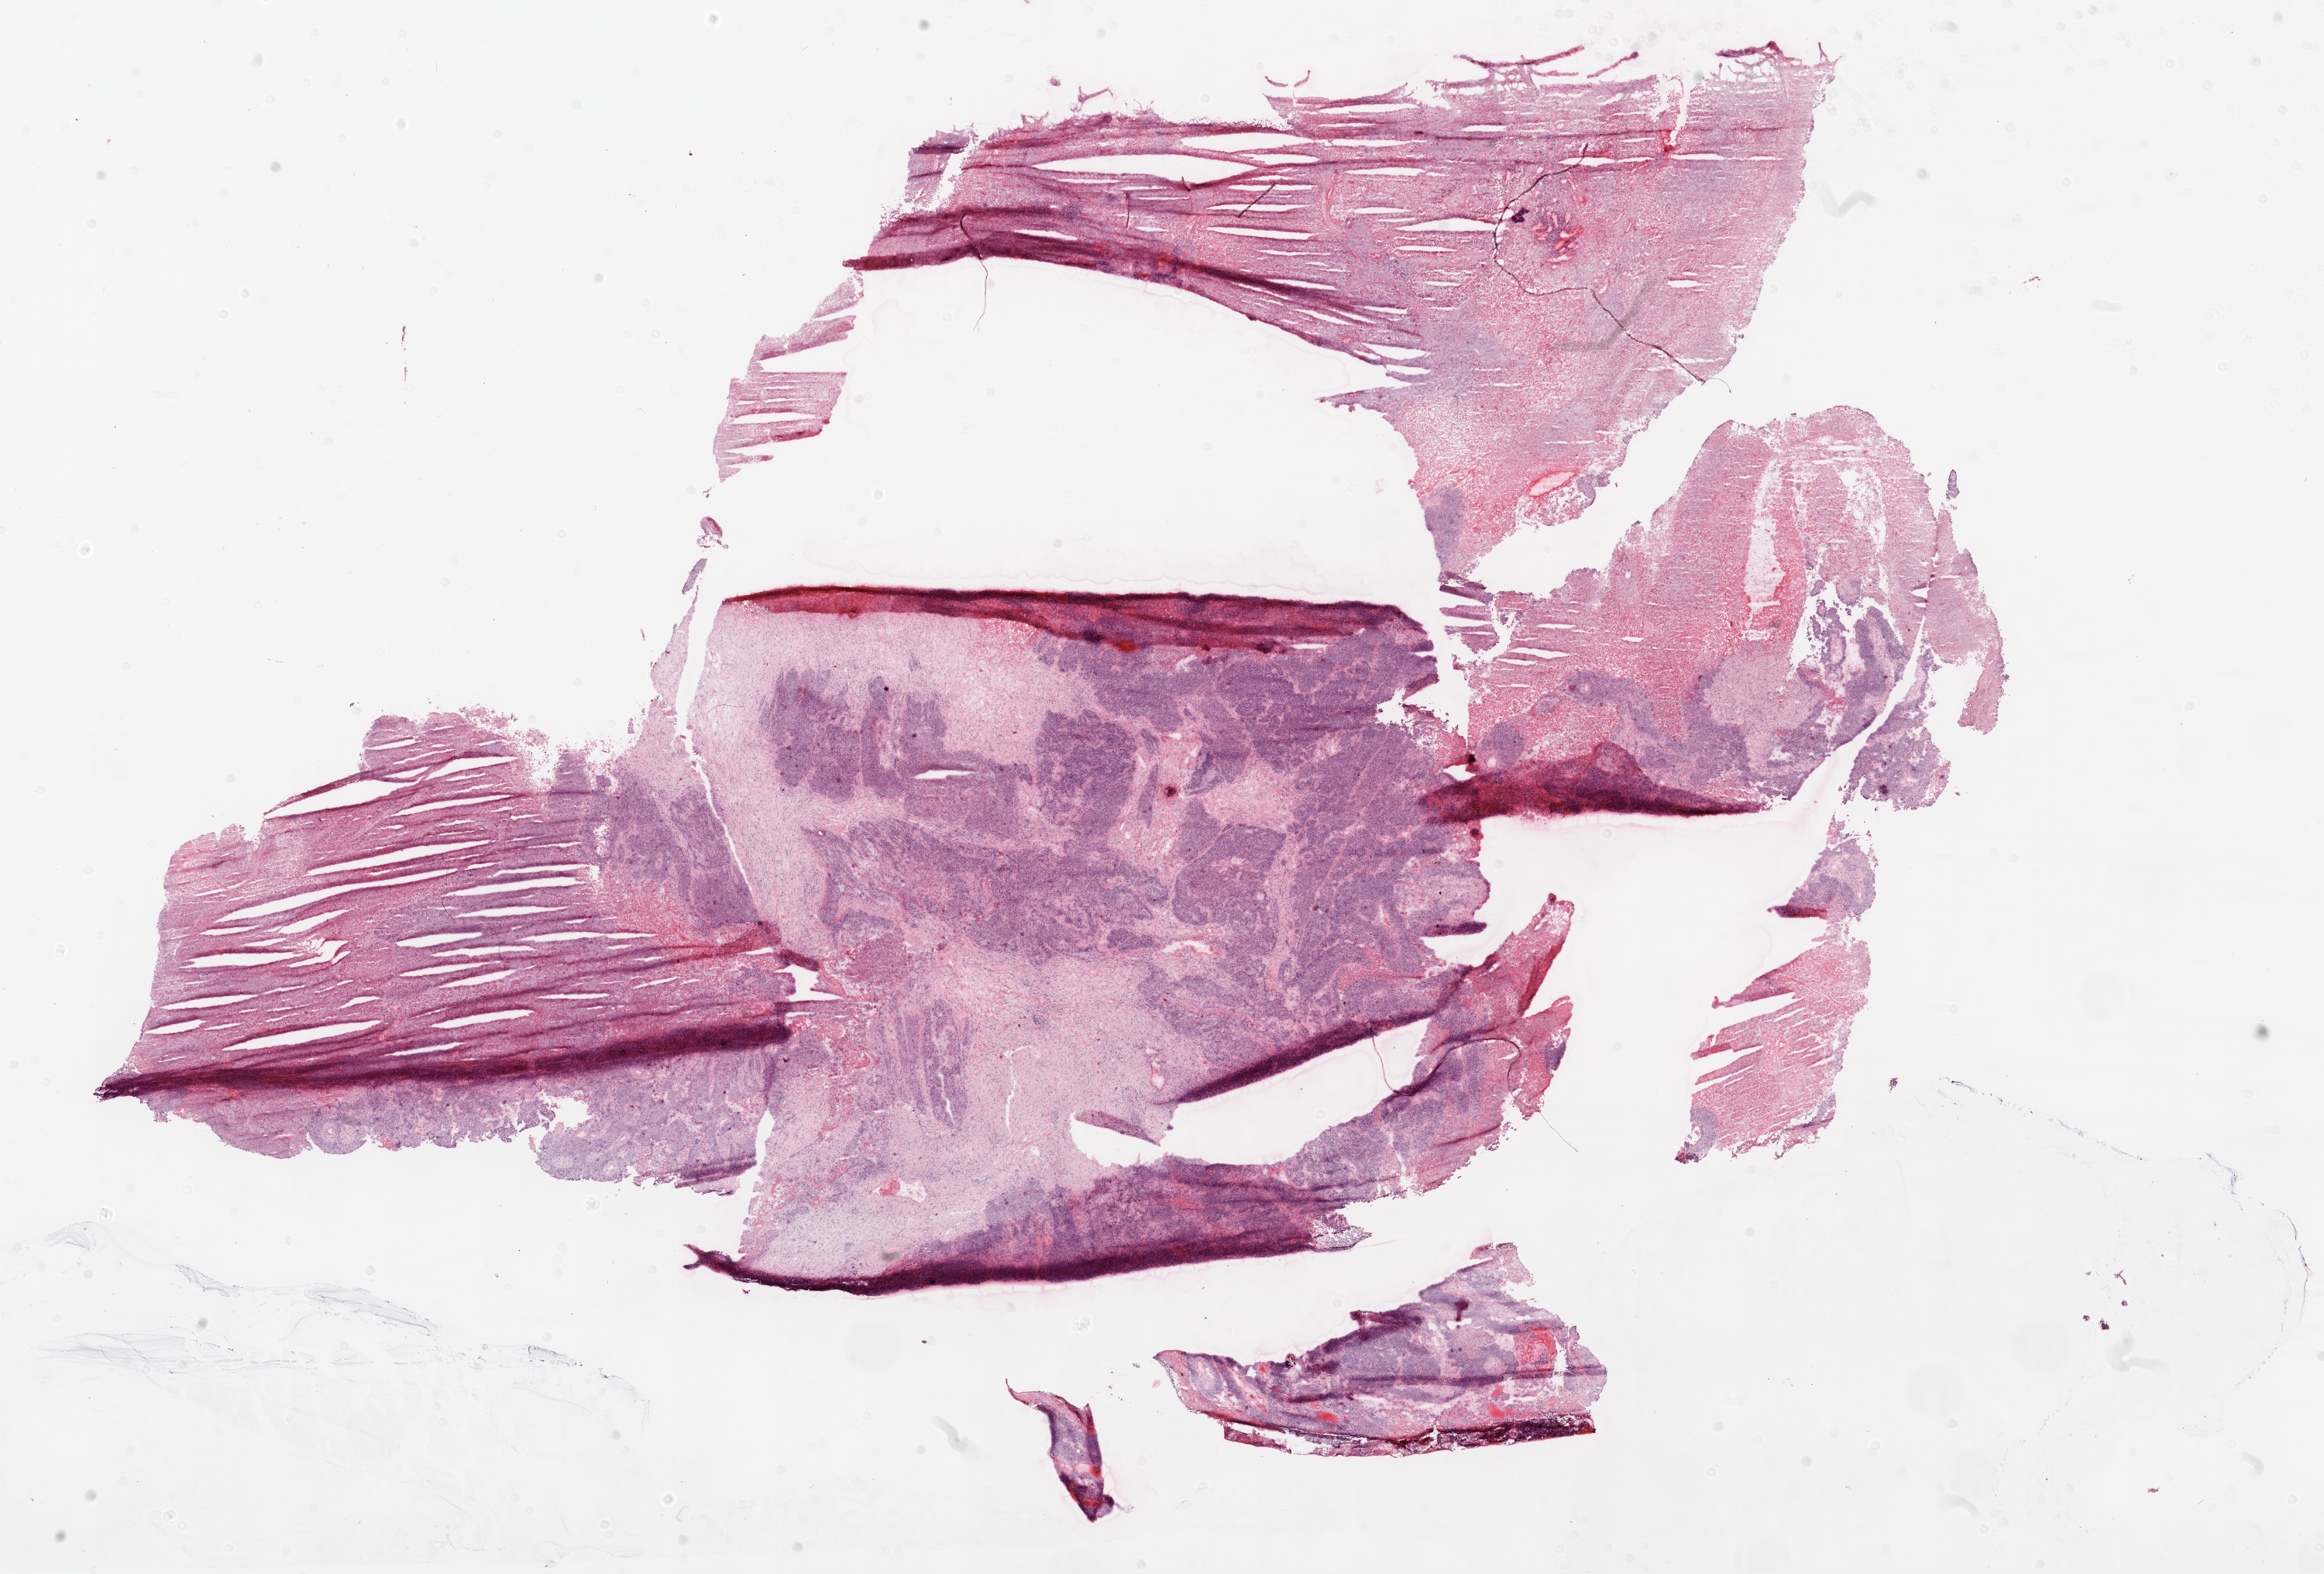
Digitized H&E-stained tissue section (whole slide) — a low-resolution overview of the entire scanned area, about 24.1 x 16.3 mm (acquisition: 20x scan); frozen section; ovary, recurrent tumour sample. Female patient; age at initial diagnosis 59 years. Slide review estimates, as recorded: tumour cells 70%, tumour nuclei 70%, normal cells 0%, stromal cells 30%, necrosis 0%. Infiltration values recorded for this section: lymphocyte infiltration 0%, monocyte infiltration 0%, neutrophil infiltration 0%.
• this section: recurrent tumour
• patient diagnosis: Serous cystadenocarcinoma, NOS